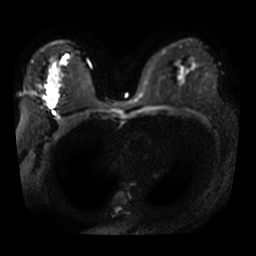
Breast MRI, one axial slice; slice 20 of 32 in the series (ordered by position); diffusion-weighted series; image 2 of 4 stored at this slice position (different b-values; order by instance number); 3 T; 256 × 256 image matrix, field of view 340 × 340 mm. Female patient.
Annotated regions visible in this slice (expert manual segmentation):
- tumour on diffusion-weighted imaging: bounding box <44,90,56,108> (left, top, right, bottom; pixels)